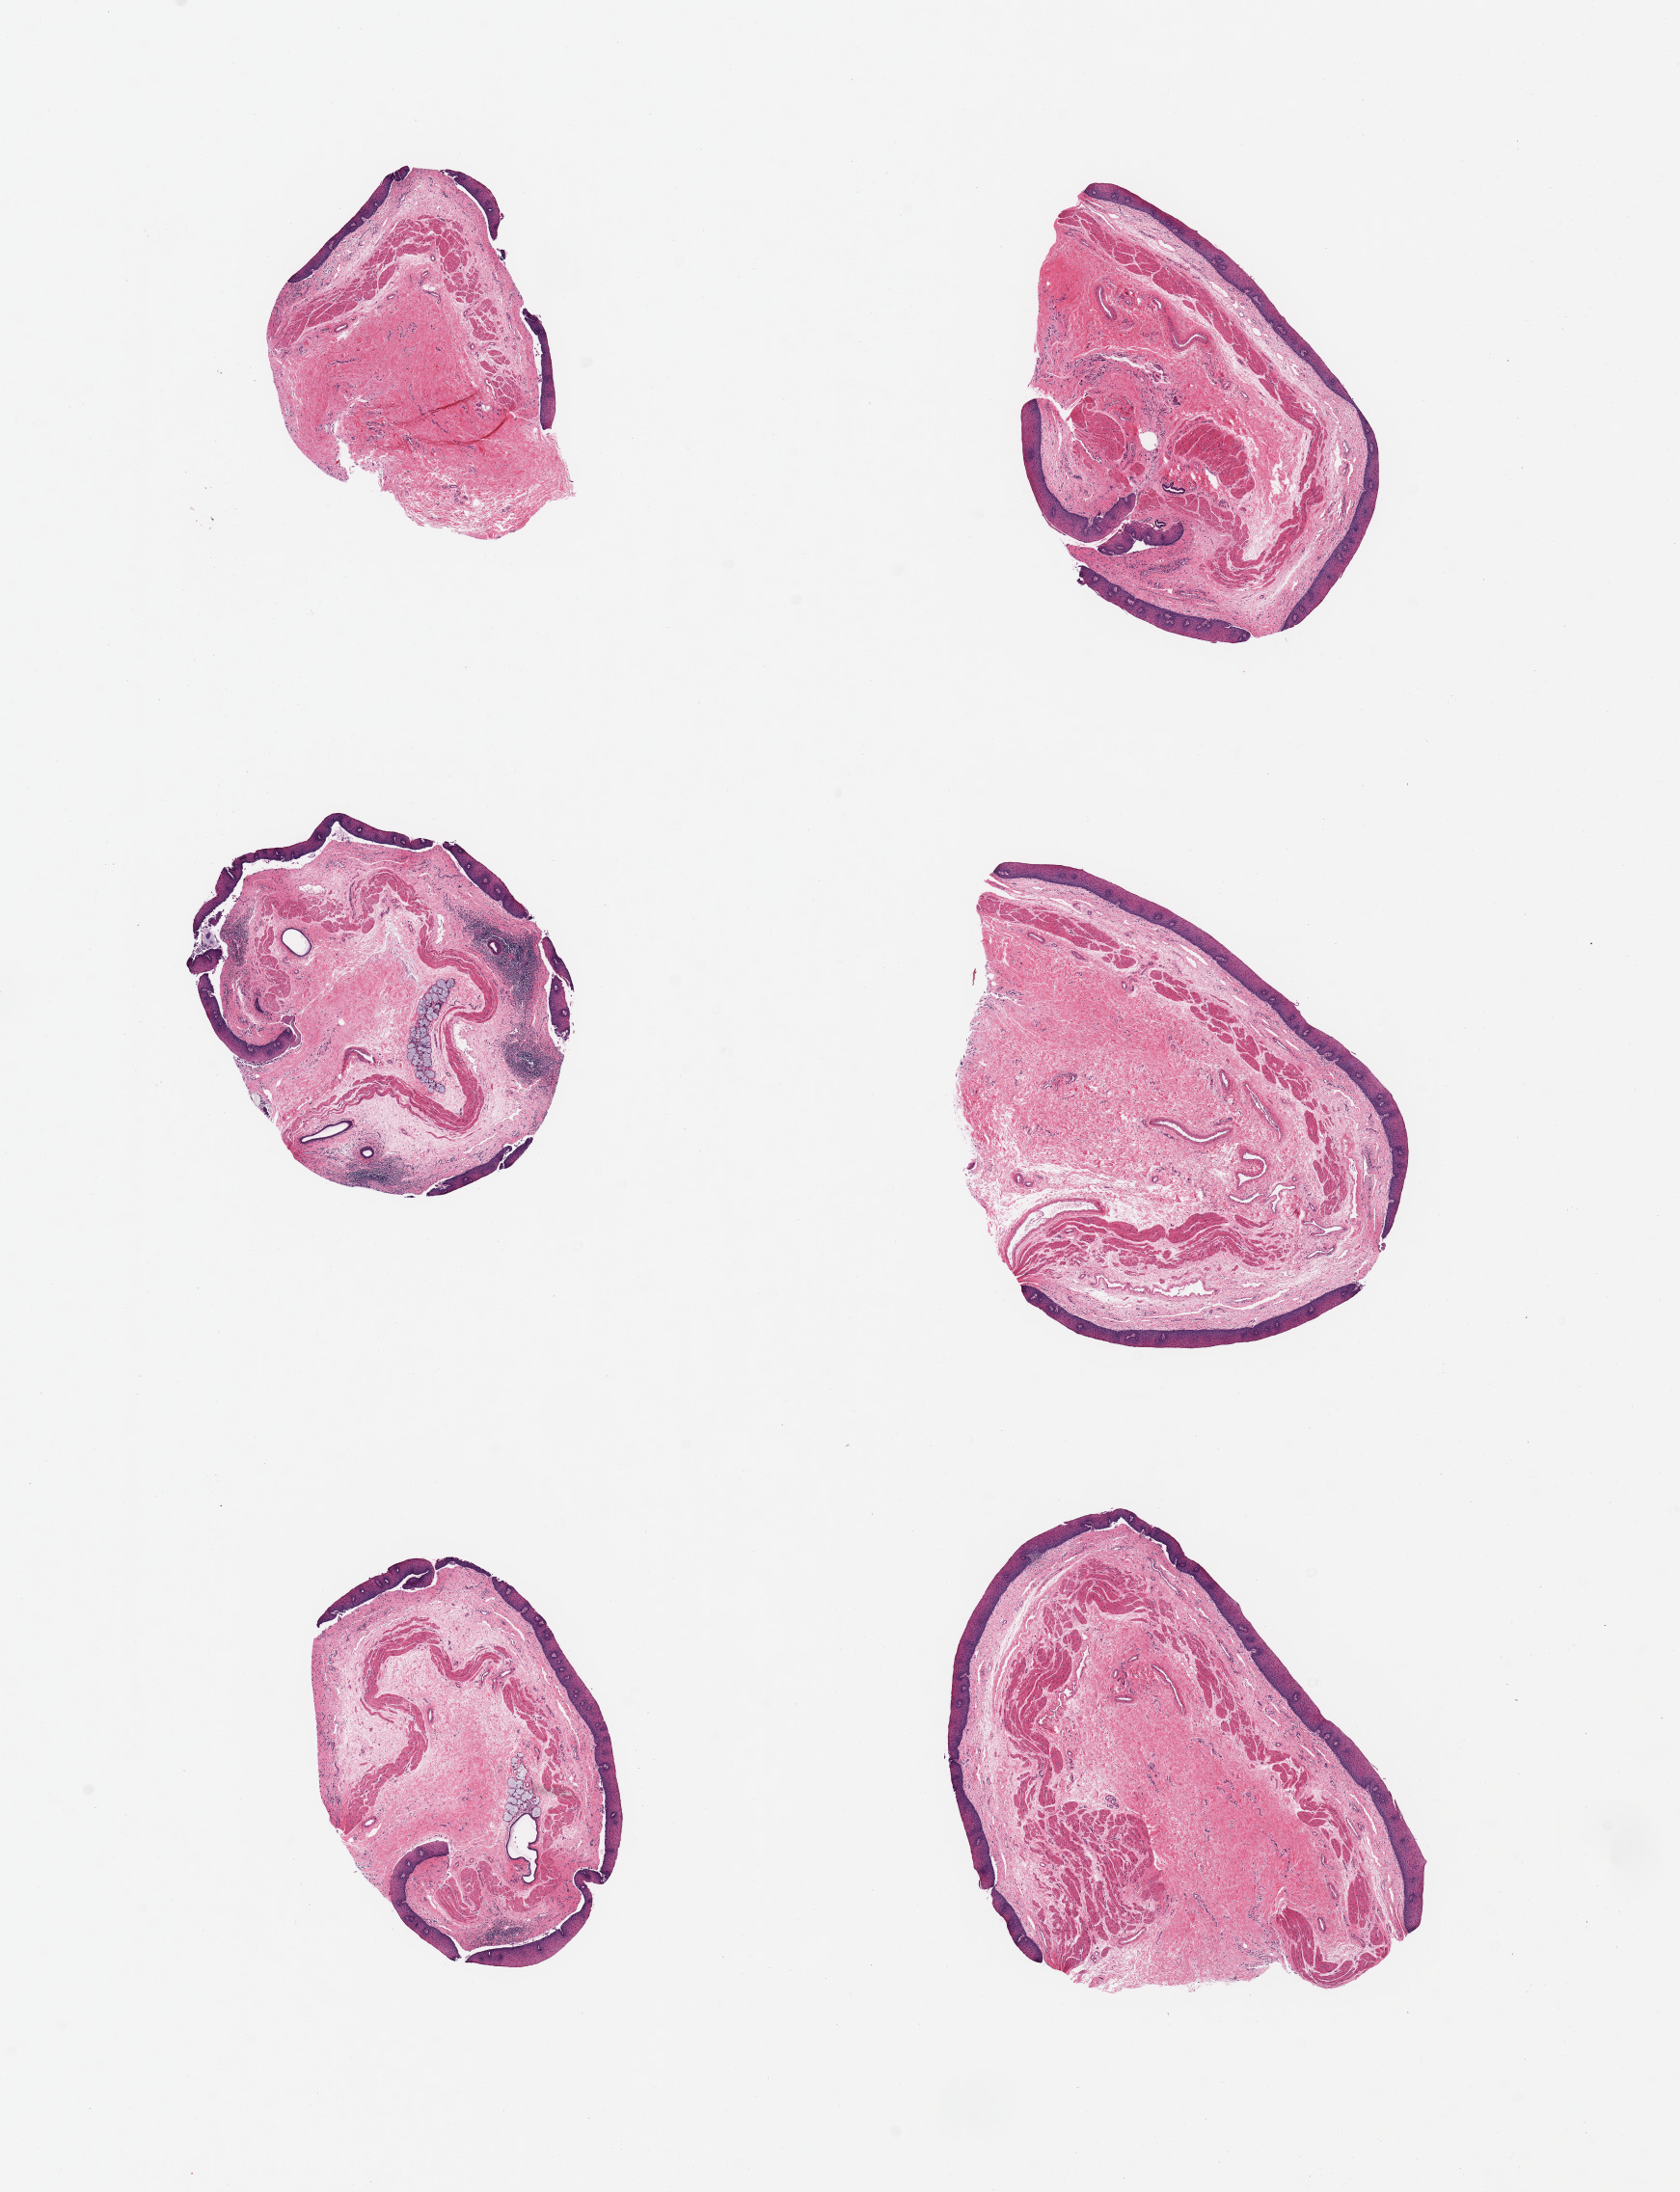
Digitized H&E-stained section — low-resolution overview of the scanned area, about 13.8 x 18.0 mm; PAXgene-fixed paraffin-embedded (PFPE) section; target tissue: gastroesophageal junction; donor tissue sample. Donor: female.
Pathologist's review note for this sample: 6 pieces; target muscularis not well represented; stratified squamous epithelium, submucosa, submucosal glands and focal submucosal lymphocytic infiltration.